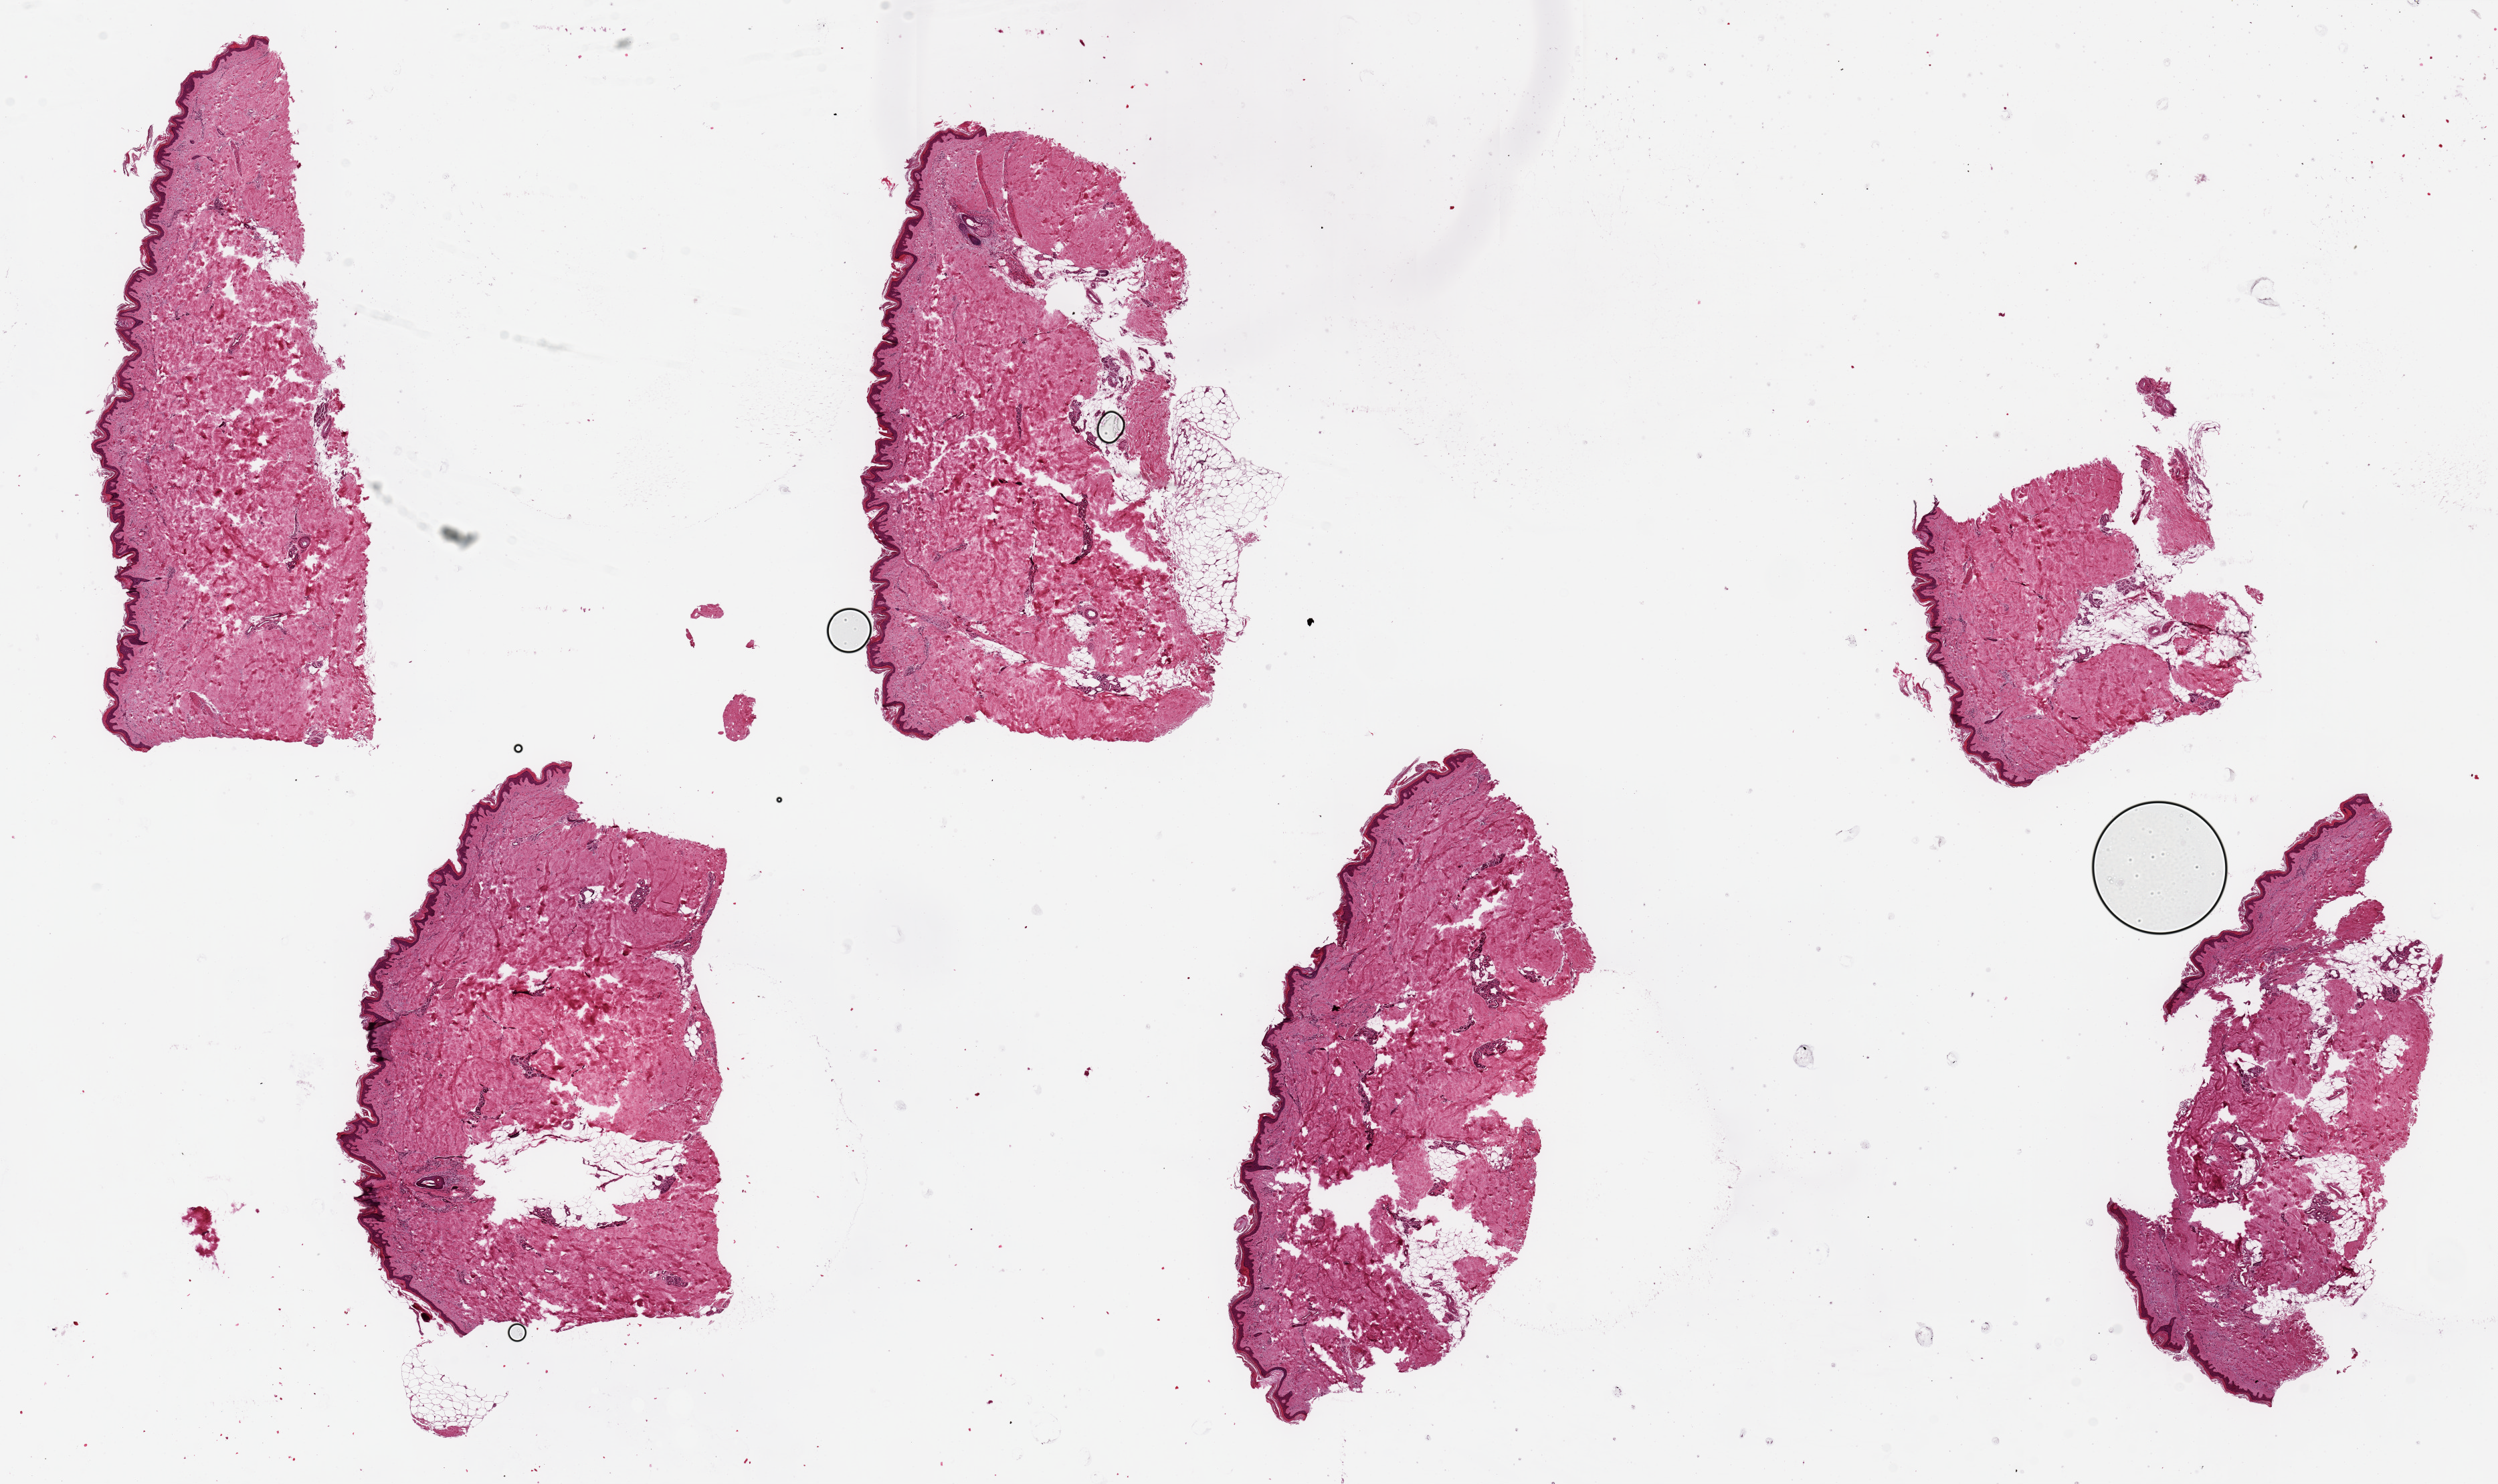
Whole-slide image, haematoxylin and eosin stain, shown as a low-resolution overview of the whole scanned area (about 29.5 x 17.6 mm); PAXgene-fixed paraffin-embedded (PFPE) section; section of skin of lower leg (target tissue); tissue donor sample. Male donor.
Pathologist's review note for this sample: 6 pieces, up to 8x3mm; squamous epithelium is ~2% of thickness.